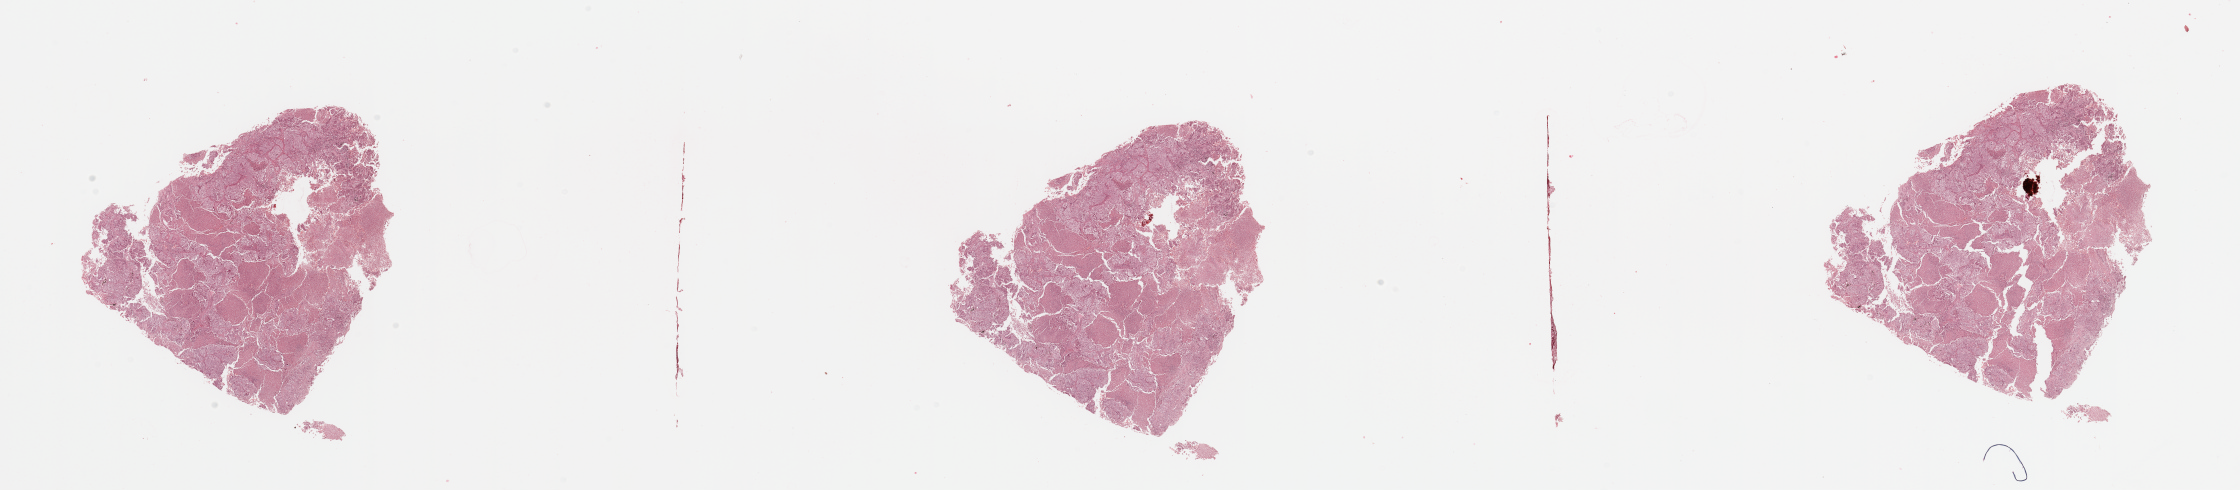
Hematoxylin and eosin (H&E) stained whole-slide image, a low-resolution overview of the entire scanned area, about 35.4 x 7.8 mm, lung, tumour tissue. Patient: male, age 71 years.
Patient diagnosis (cohort enrolment): squamous cell carcinoma (lung).